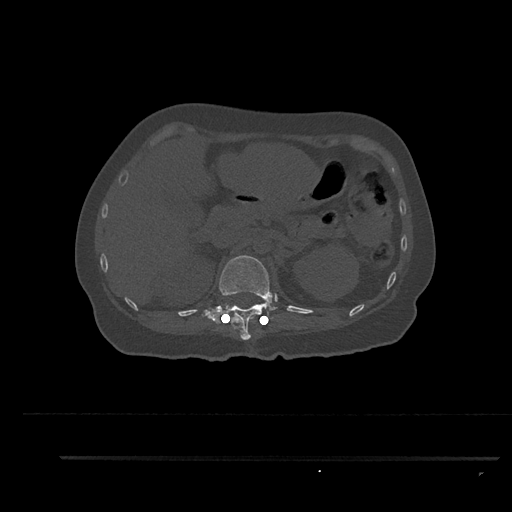
CT including the spine, one axial slice; slice 252 of 797 in the series (ordered by position); reconstruction kernel Br40s/3; bone window (W 1800 / L 400 HU); 0.5 mm slice thickness; 512 × 512 image matrix, field of view 408 × 408 mm. Patient: female, 44 years. From the clinical record (not read from this slice): primary cancer: renal; vertebrae with lytic lesions (as recorded): L1.
Annotated regions visible in this slice (semi-automatic segmentation, software-assisted and operator-edited):
- T12 vertebra: bounding box <202,255,273,340> (left, top, right, bottom; pixels)